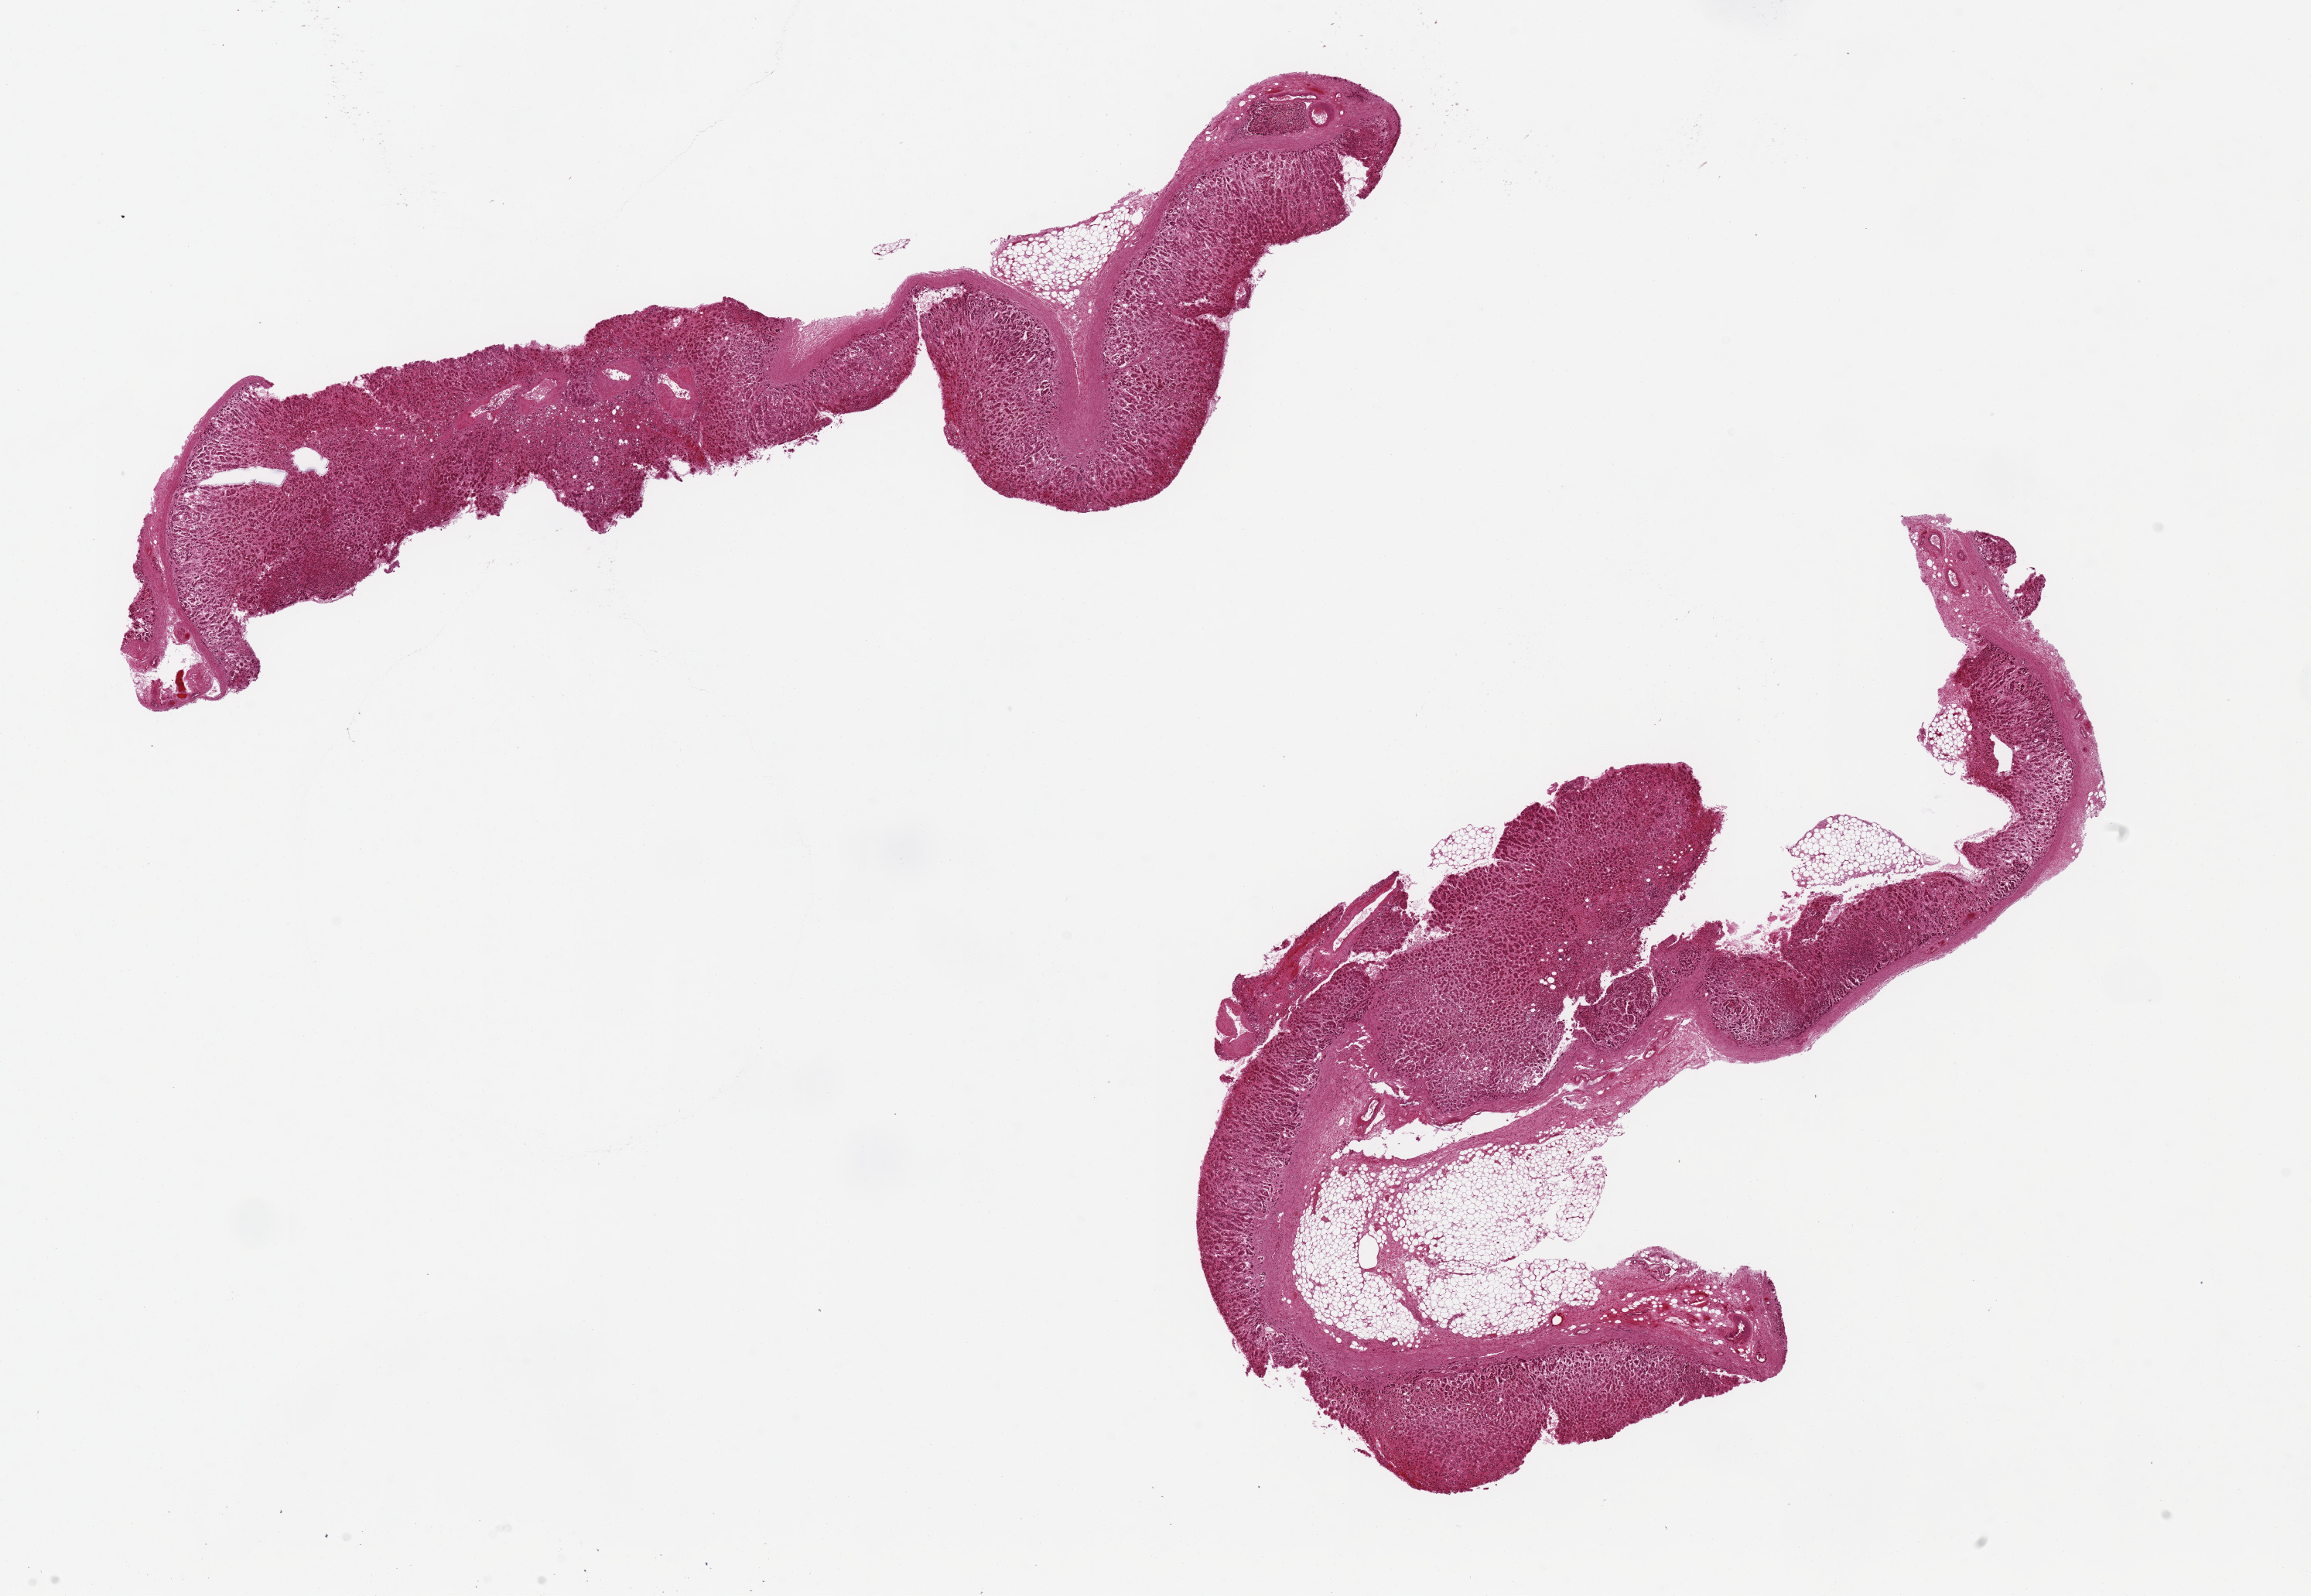
Digitized haematoxylin and eosin-stained section, brightfield — shown as a low-resolution overview of the whole scanned area (about 23.6 x 16.3 mm). PAXgene-fixed paraffin-embedded (PFPE) section. Target tissue: adrenal gland. Donor tissue sample.
Review note (as recorded): 2 pieces 14x2 & 11x6 mm; ~20% adherent adipose.